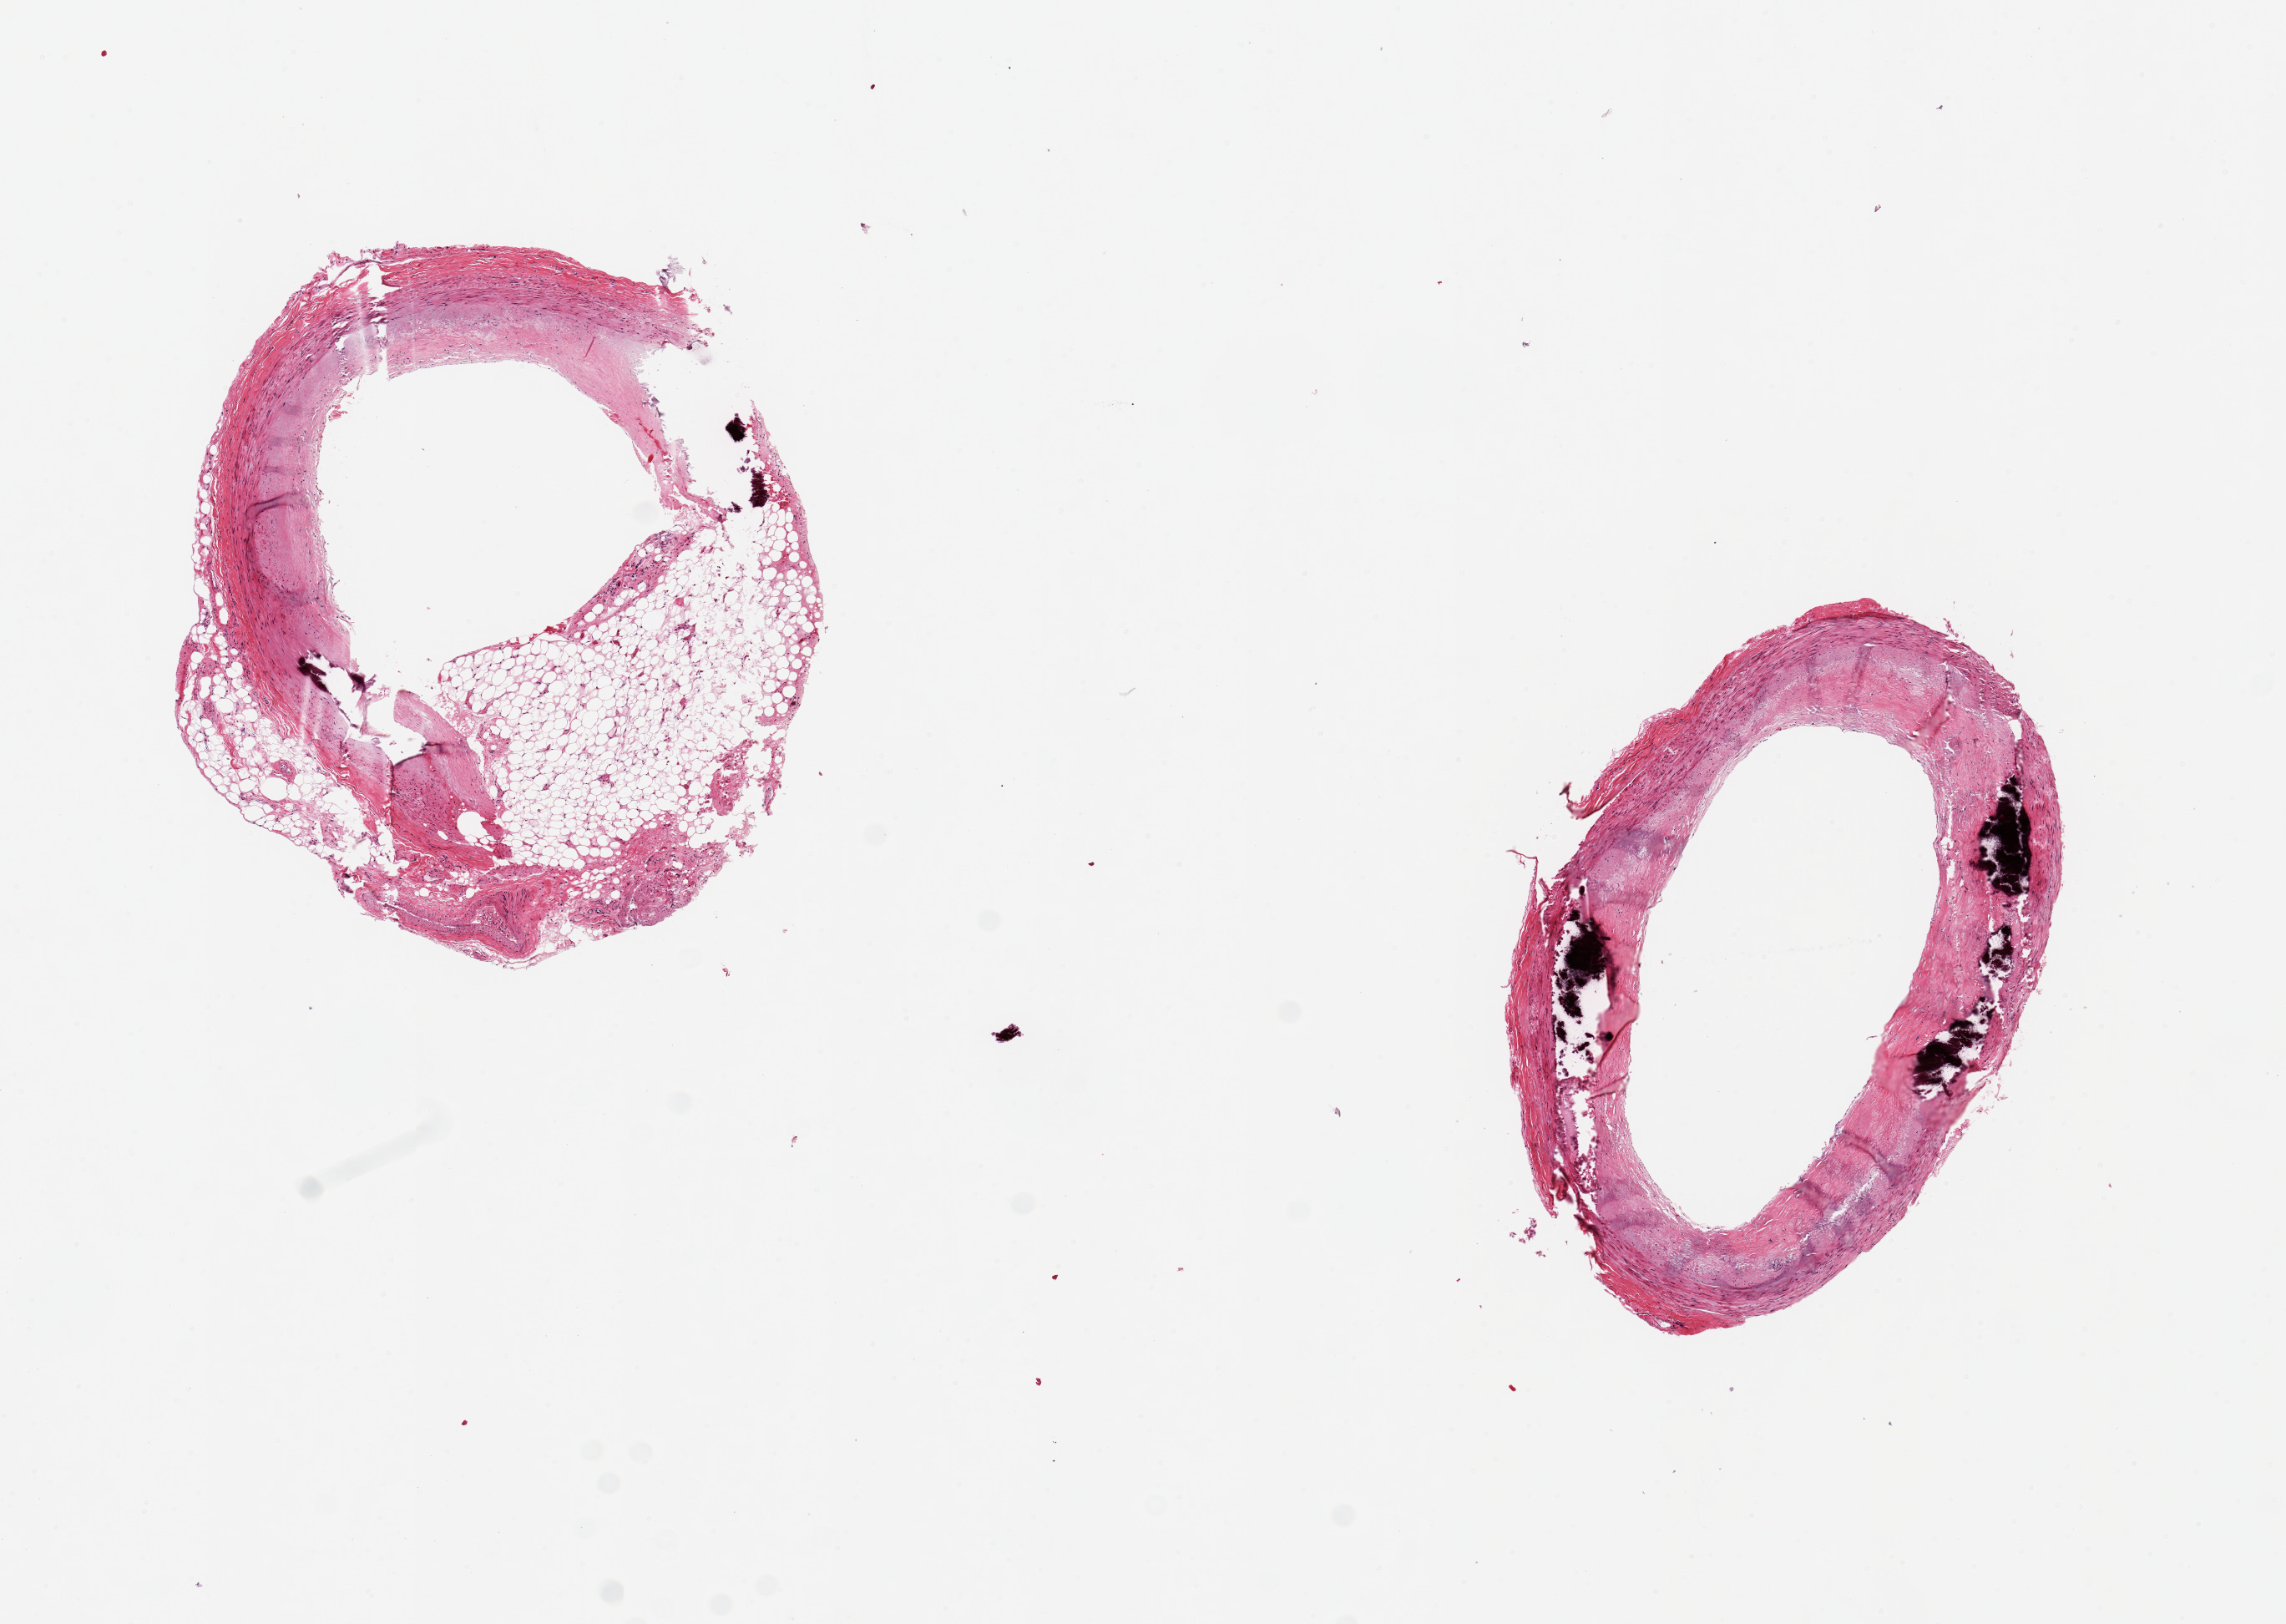
Digitized H&E-stained section, whole scanned area (about 10.8 x 7.7 mm) shown as a low-resolution overview. PAXgene-fixed, paraffin-embedded tissue. Sampled site (target tissue): coronary artery. Donor tissue sample. Donor sex: male.
Pathologist's review note for this sample: 2 pieces, 3.5x3 & 4x3mm; Both pieces heavily calcified; one has 1x1.7 mm adipose replacing wall.